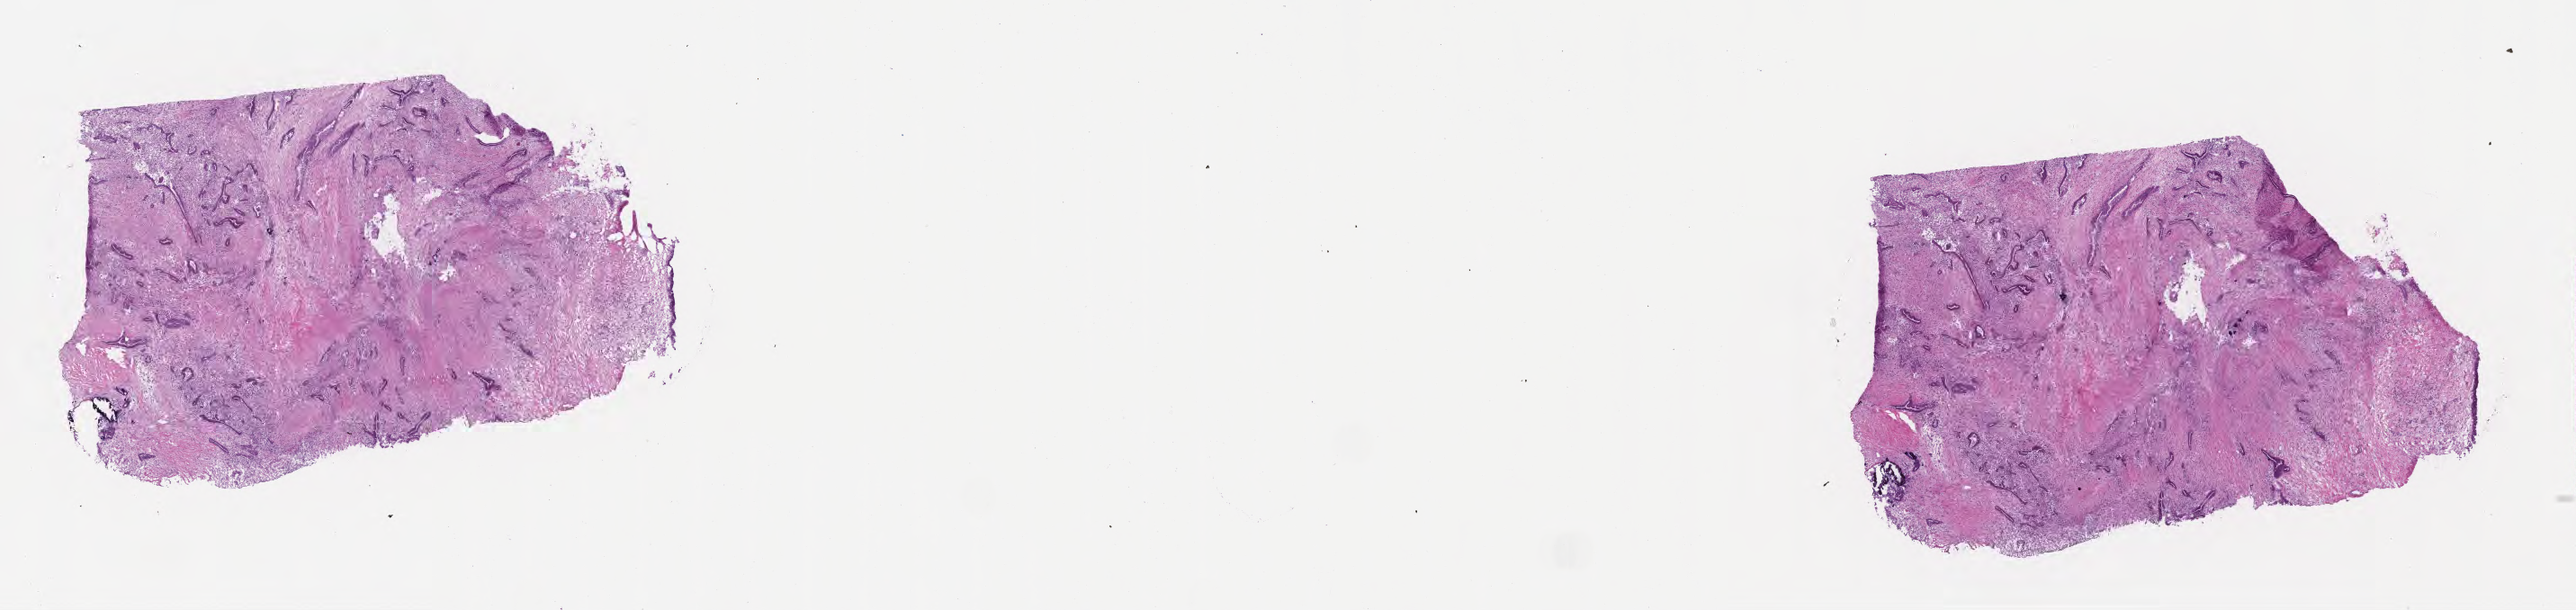
Digitized H&E-stained section — a low-resolution overview of the entire scanned area, about 23.1 x 5.5 mm; cryosection; specimen: primary tumor; anatomic site: neck of pancreas. Patient: female, age at initial diagnosis 80 years. Tumor grade: G2 (moderately differentiated). Composition of this section per pathologist review: tumor cells 70%, tumor nuclei 70%, stromal cells 24%, necrosis 0%, normal cells 6%. Inflammatory infiltration, as recorded: lymphocyte infiltration 6%, monocyte infiltration 3%, neutrophil infiltration 8%.
* histologic diagnosis: Infiltrating duct carcinoma, NOS
* section: top of the tissue portion
* AJCC pathologic stage: Stage IIB